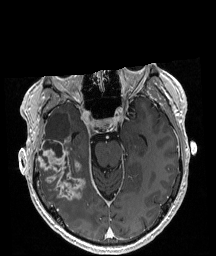
Brain MRI from a brain-tumour surgery series, one axial slice; position 126 of 208 along the scan axis; T1-weighted post-contrast; 1 mm slice thickness; 216 × 256 image matrix, field of view 211 × 250 mm. From the clinical record (not read from this slice): histopathology: Astrocytoma; WHO grade: 4; IDH mutation: yes.
Structures marked on this image (outlined manually by an expert reader):
- tumour: bounding box <37,135,86,200> (left, top, right, bottom; pixels)